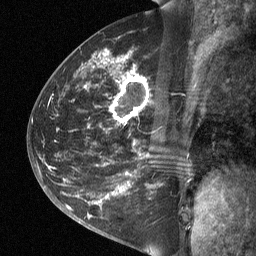
Breast MRI (dynamic contrast-enhanced), one sagittal slice. Position 32 of 64 along the scan axis. Dynamic contrast-enhanced study with each time point stored as its own series, time point 2 of 3 at this slice position (early post-contrast, ordered by acquisition time). 1.5 T. TE 4.8 ms, TR 27 ms. 2 mm slice thickness. 256 × 256 image matrix, field of view 200 × 200 mm. Female patient, age 42 years. Case-level facts recorded for this patient, not image findings: setting: breast cancer imaged before/during neoadjuvant chemotherapy; receptor status: triple-negative.
Annotated regions visible in this slice (semi-automatically segmented with operator editing):
- analysis volume of interest (the breast-tissue region the enhancement analysis was run in; not a lesion): box from (x=49, y=45) to (x=197, y=197) px
- tumour enhancement mask (voxels above the 90 % enhancement threshold inside the analysis volume of interest): (x=116, y=78)–(x=145, y=114)